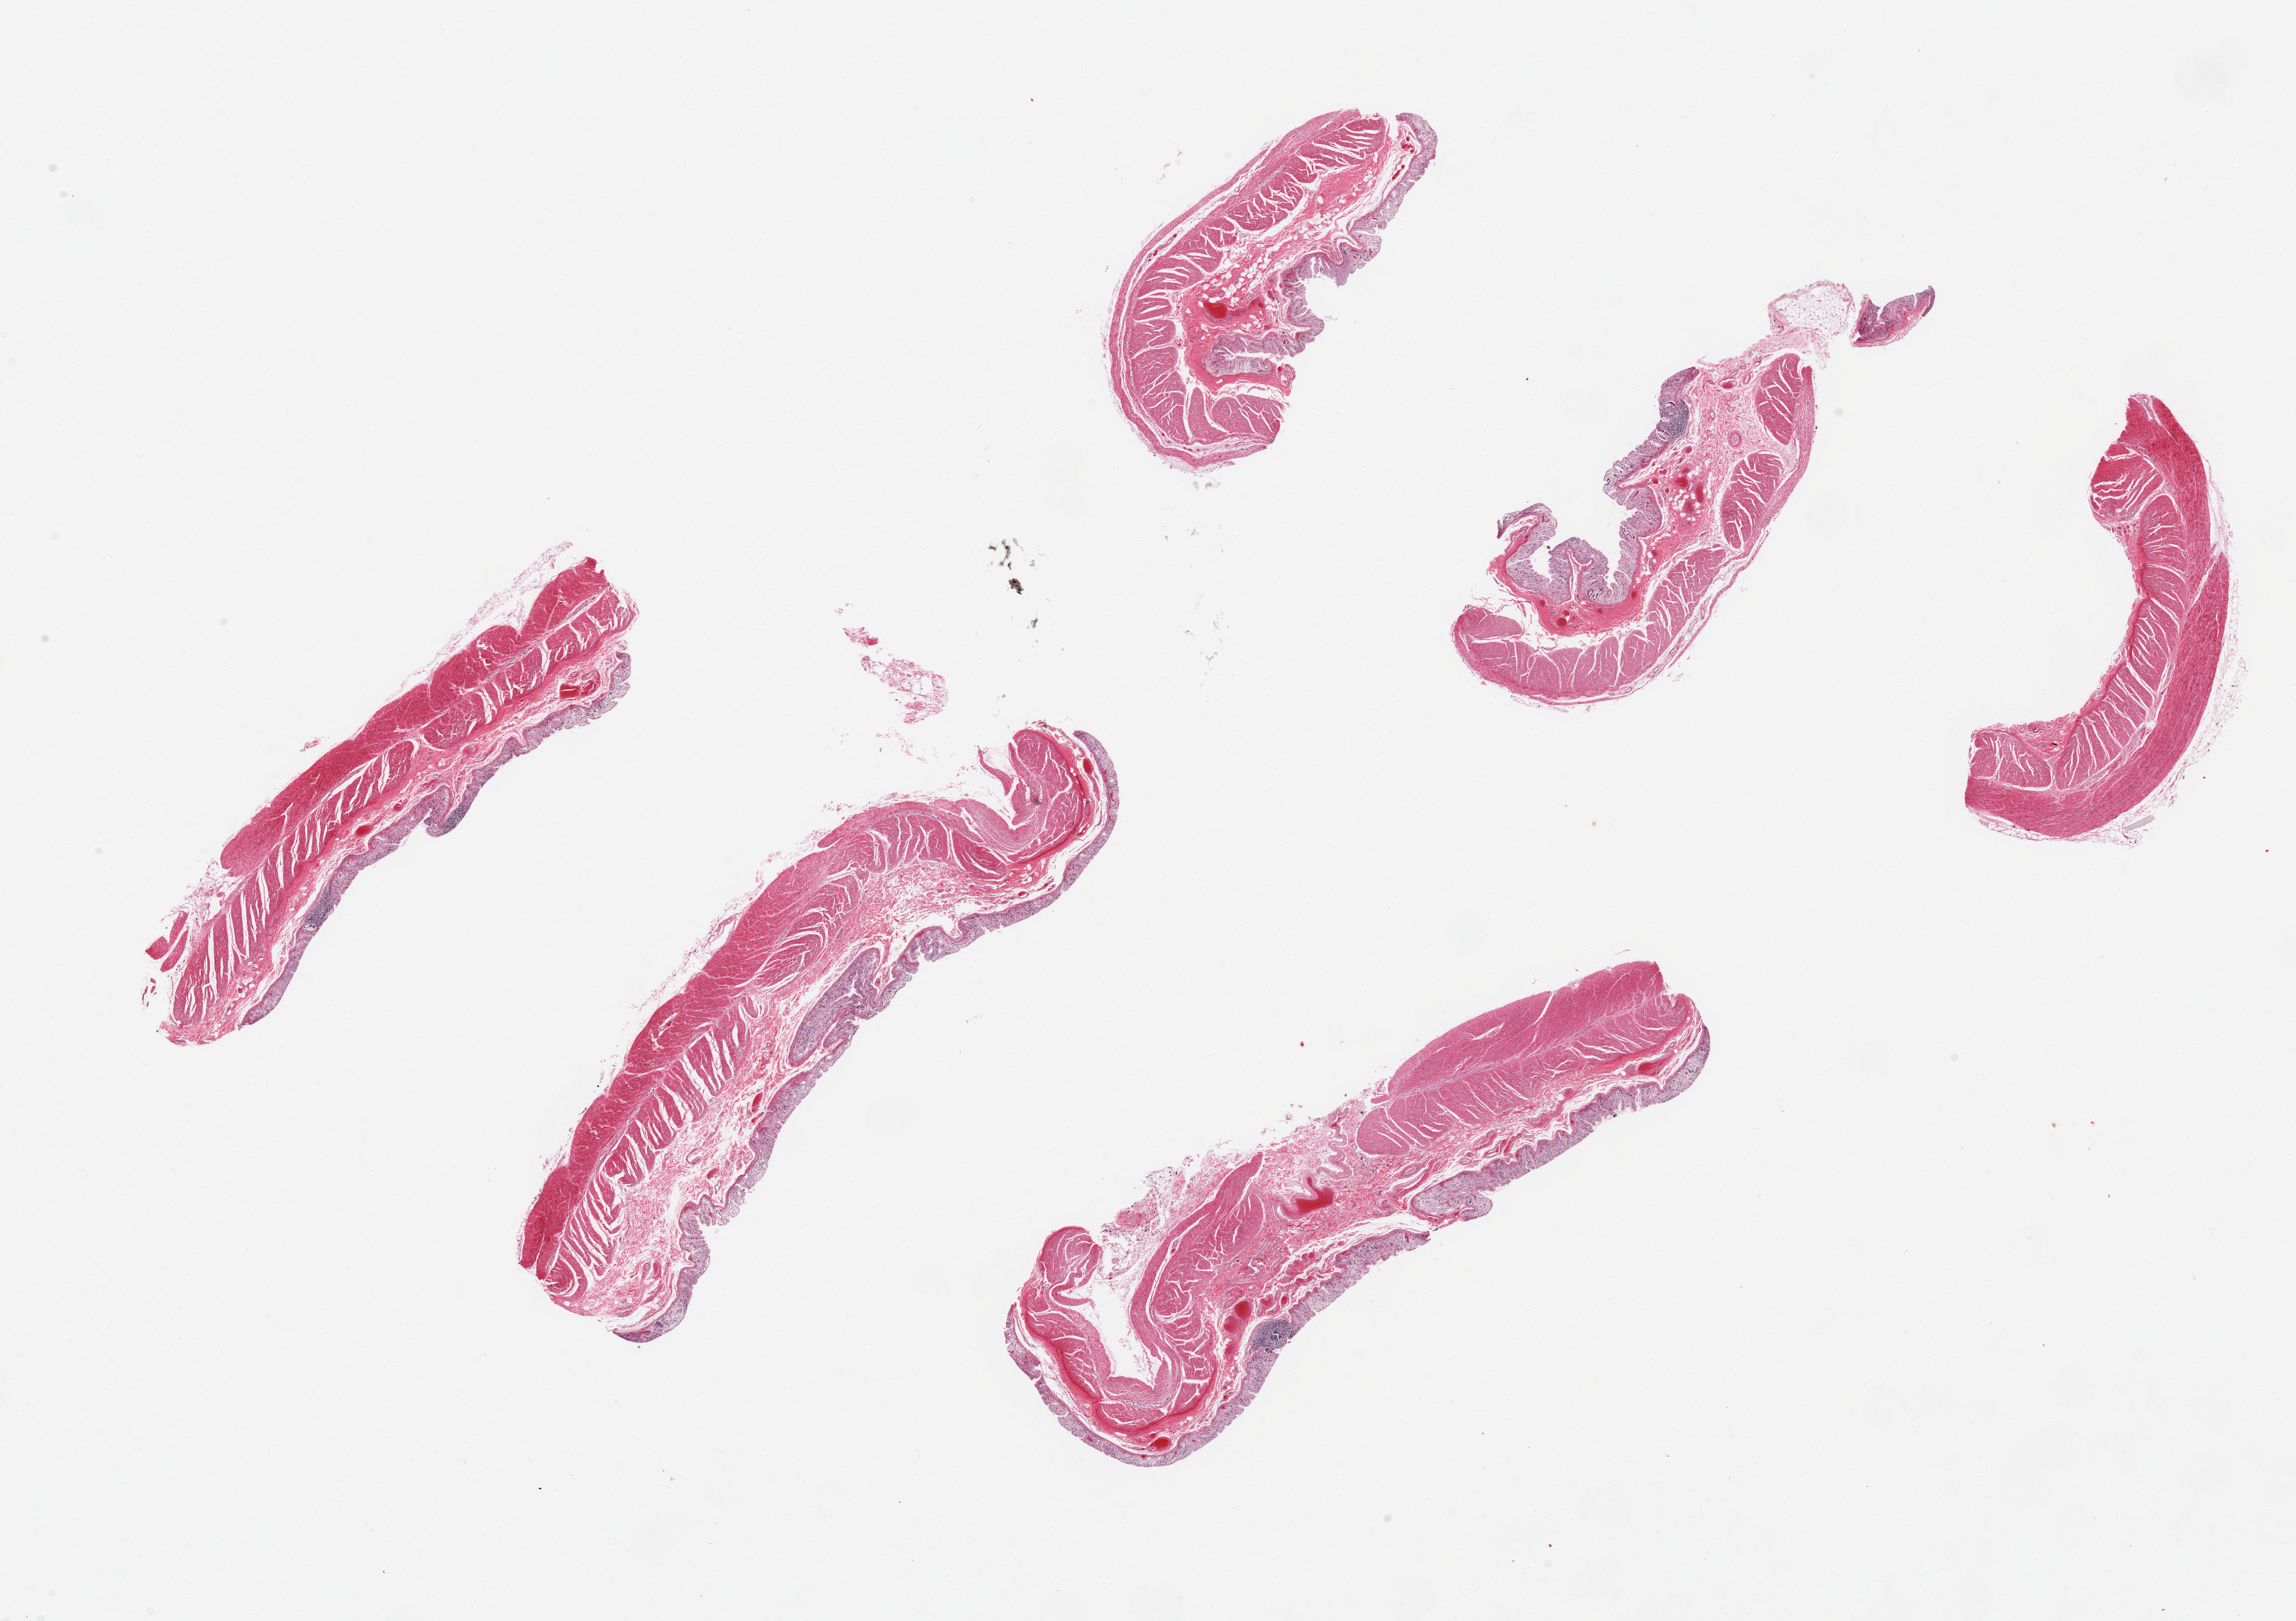
Whole-slide image, haematoxylin and eosin stain, whole scanned area (about 25.6 x 18.1 mm) shown as a low-resolution overview. PAXgene-fixed paraffin-embedded (PFPE) section. Sampled site (target tissue): transverse colon. Tissue donor sample. Female donor.
Review note (as recorded): 6 pieces up to 8x2 mm; mucosa largely autolyzed; muscle mildly autolyzed.